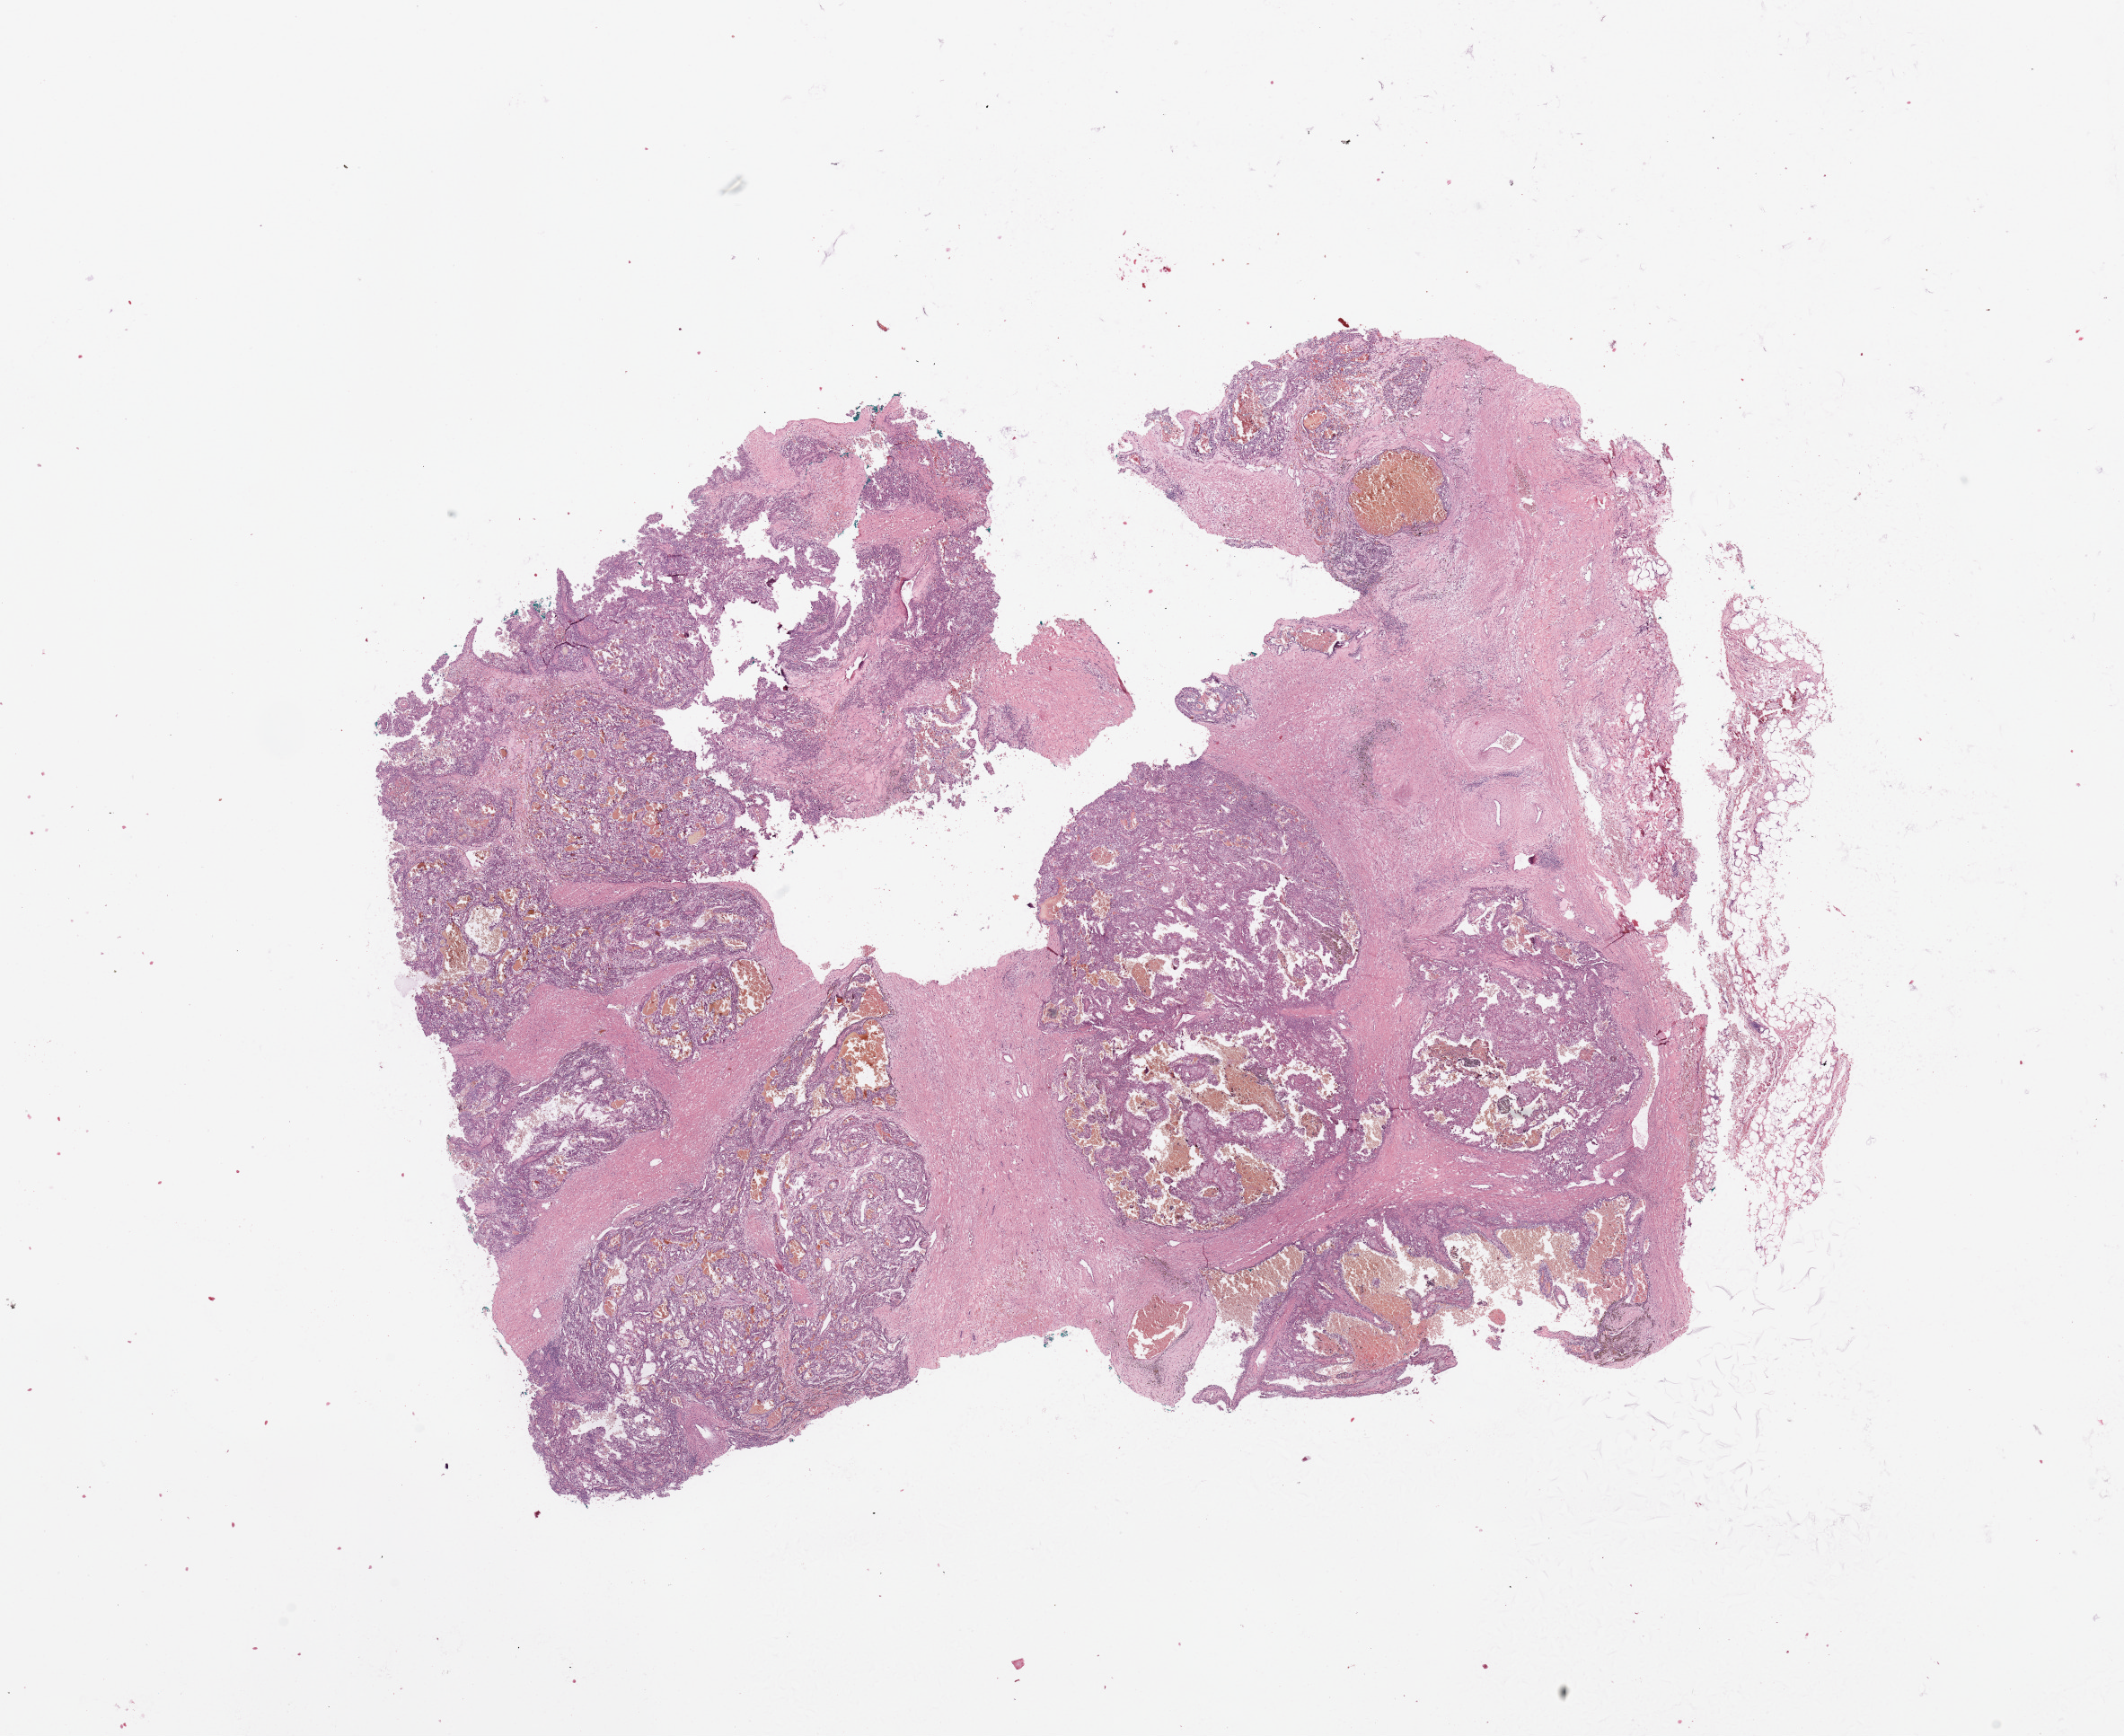
Hematoxylin and eosin (H&E) stained whole-slide image, whole scanned area (about 18.7 x 15.3 mm) shown as a low-resolution overview; tumour tissue sample, kidney. Patient: male, age 45 years. Histologic grade: G2 (moderately differentiated).
Primary tumour site (as recorded): middle. Histologic diagnosis: Renal cell carcinoma, NOS. AJCC pathologic stage: II.